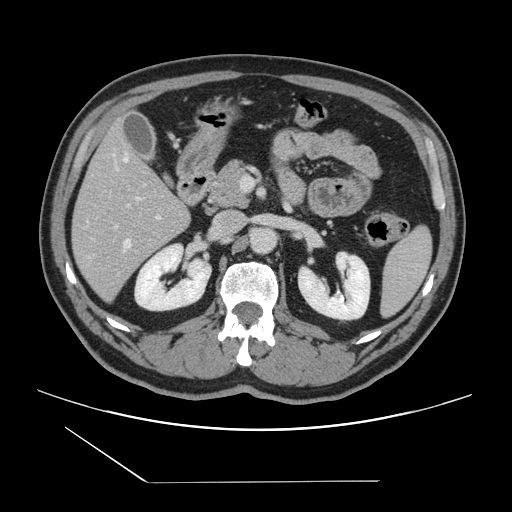
Contrast-enhanced abdominal CT, one axial slice; slice 68 of 157 in the series (ordered by position); intravenous contrast given; soft-tissue window (W 400 / L 40 HU); 512 × 512 image matrix, field of view 407 × 407 mm. Male patient, age 61 years. From the clinical record (not read from this slice): diagnosis: colorectal cancer liver metastases, imaged before liver resection; multiple liver metastases: yes; largest metastasis: 5.5 cm.
Outlined on this slice (expert manual segmentation):
- hepatic veins: bounding box (x1, y1, x2, y2) in pixels: (123, 155, 139, 251)
- liver: (73, 126, 189, 300)
- planned liver remnant (the part of the liver to remain after resection): (75, 125, 178, 218)
- portal vein (with intrahepatic branches): (115, 167, 161, 228)